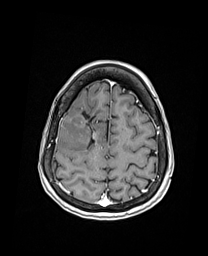
Brain MRI from a brain-tumour surgery series, one axial slice; T1-weighted post-contrast; 1 mm slice thickness; 208 × 256 image matrix. From the clinical record (not read from this slice): histopathology: Oligodendroglioma; WHO grade: 3; IDH mutation: yes.
Outlined on this slice (expert manual segmentation):
- previous resection cavity: bounding box (x1, y1, x2, y2) in pixels: (72, 109, 99, 141)